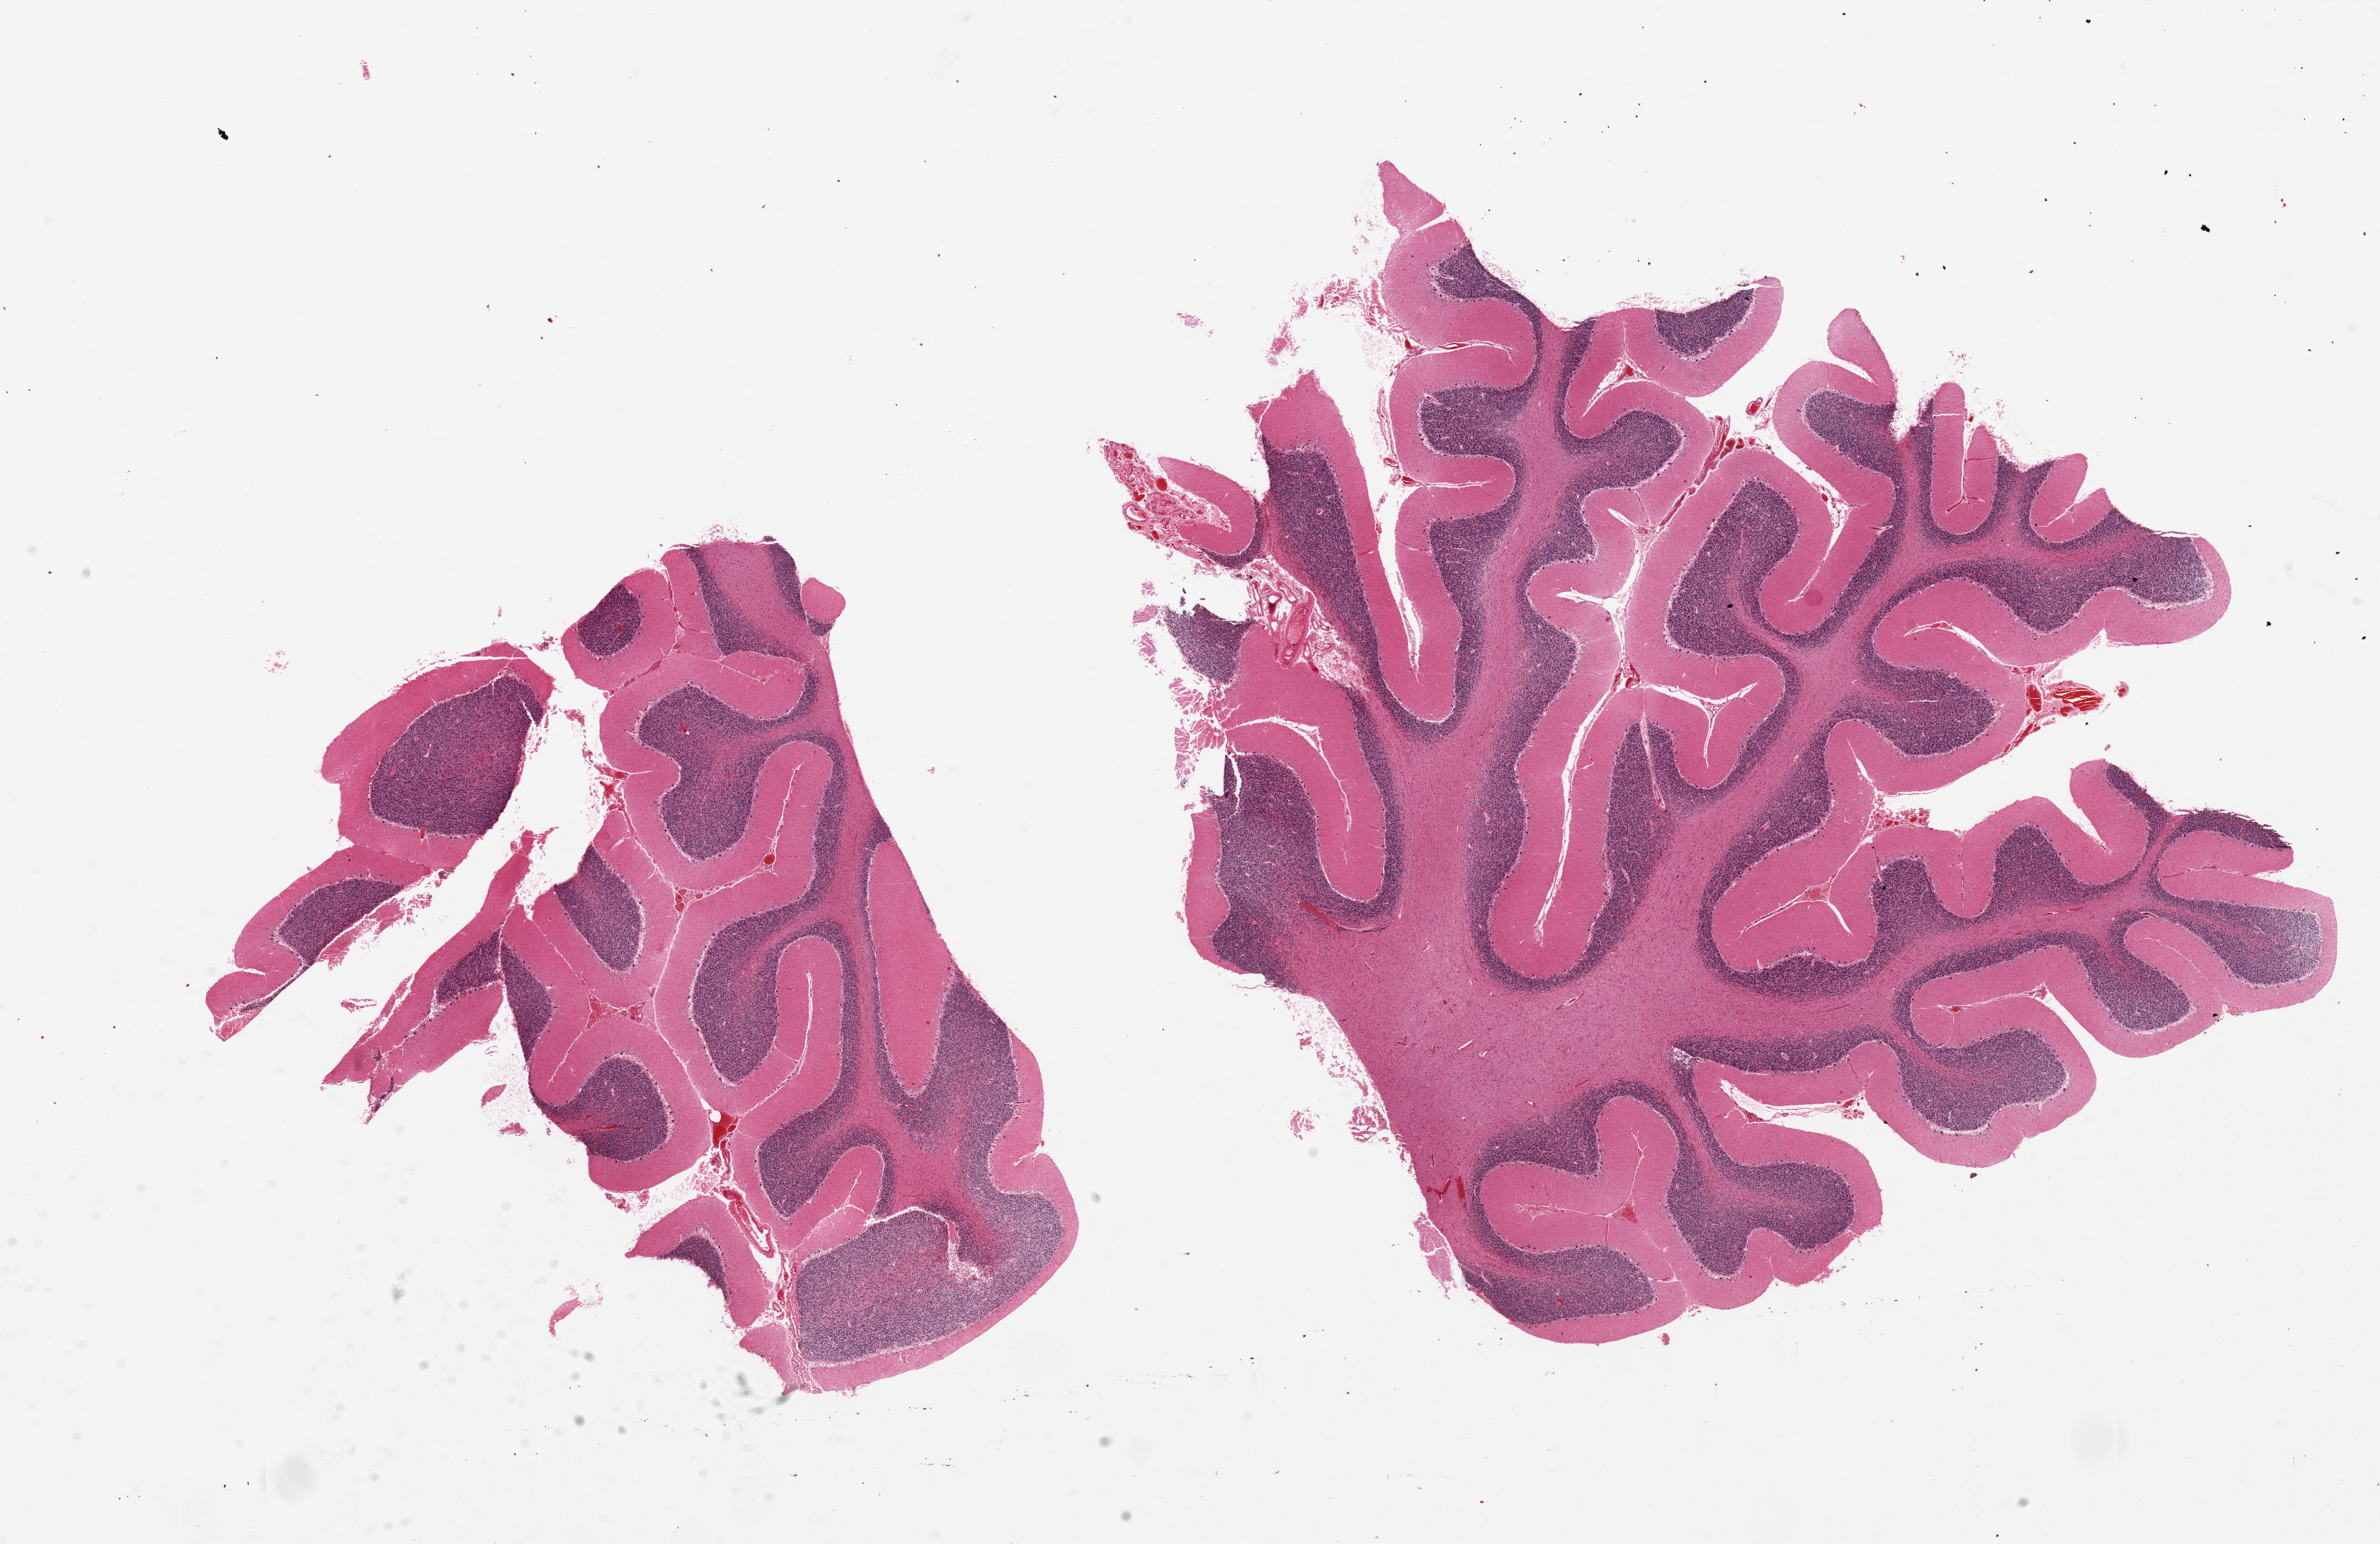
Whole-slide image, H&E stain — whole scanned area (about 26.6 x 17.2 mm, acquisition: 20x scan) shown as a low-resolution overview. PAXgene-fixed paraffin-embedded (PFPE) section. Sampled site (target tissue): cerebellum. Tissue donor sample.
Reviewer comment on this tissue sample: 2 pieces, Purkinje cells, no evidence of hypoxic damage.